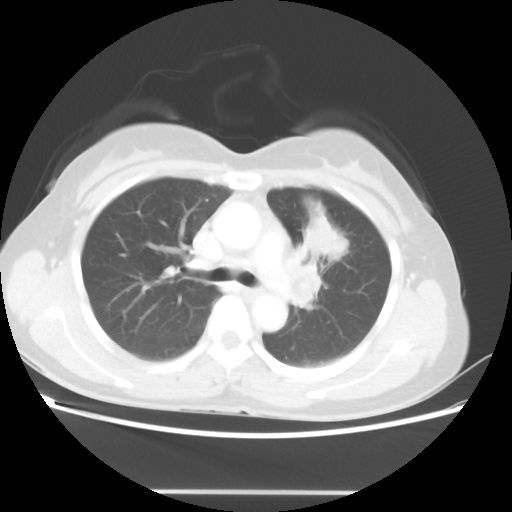
Chest CT, one axial slice. Slice 30 of 46 in the series (ordered by position). Reconstruction kernel STANDARD. Lung window (W 1500 / L -600 HU). 5 mm slice thickness. 512 × 512 image matrix, field of view 360 × 360 mm. Patient: female, 50 years. From the clinical record (not read from this slice): clinical TNM (as recorded): T1c N1 M0.
Annotated regions visible in this slice (rectangle marked by the reading radiologist):
- lung tumour (recorded histology: adenocarcinoma): box from (x=303, y=208) to (x=348, y=256) px